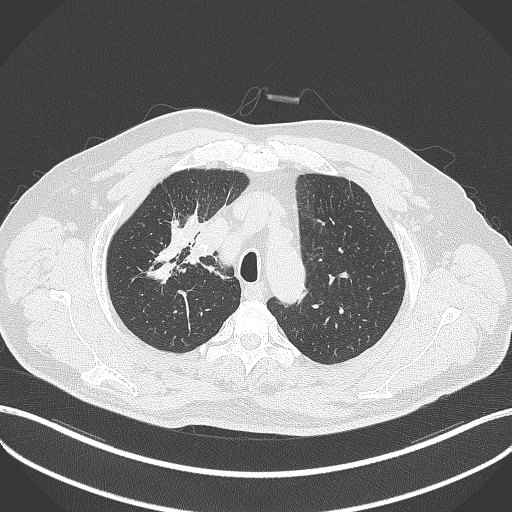
Chest CT, one axial slice; slice 310 of 411 in the series (ordered by position); lung window (W 1500 / L -600 HU); 1 mm slice thickness; 512 × 512 image matrix, field of view 400 × 400 mm. Male patient, age 60 years. Case-level facts recorded for this patient, not image findings: clinical TNM (as recorded): T1b N1 M0.
Structures marked on this image (bounding box drawn by a radiologist):
- lung tumour (recorded histology: squamous cell carcinoma): bounding box [x1, y1, x2, y2] px = [181, 245, 213, 271]